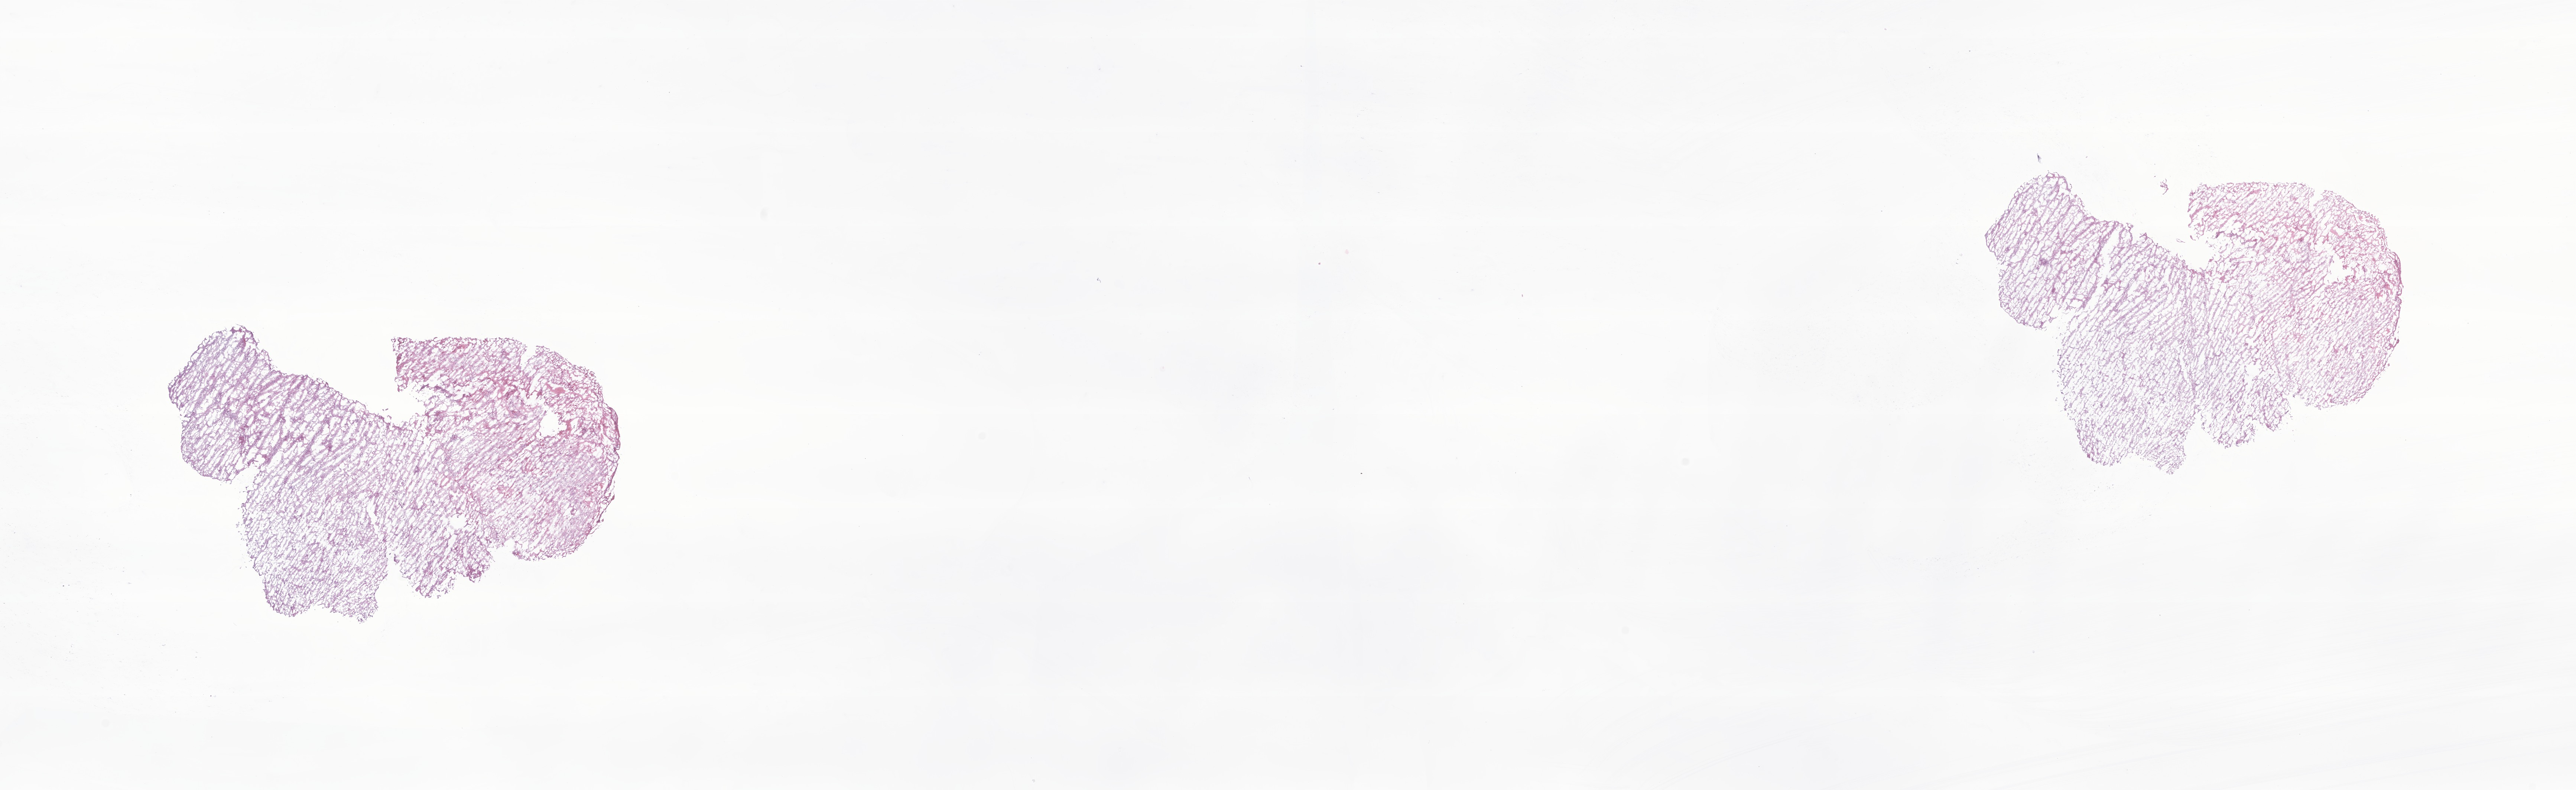
Whole-slide image, haematoxylin and eosin stain of tumor tissue from the brain, whole scanned area (about 29.2 x 9.0 mm) shown as a low-resolution overview; frozen section. Female patient, age 173 months (14 years 5 months).
Diagnosis (ICD-O-3 morphology term): Neoplasm, uncertain whether benign or malignant.